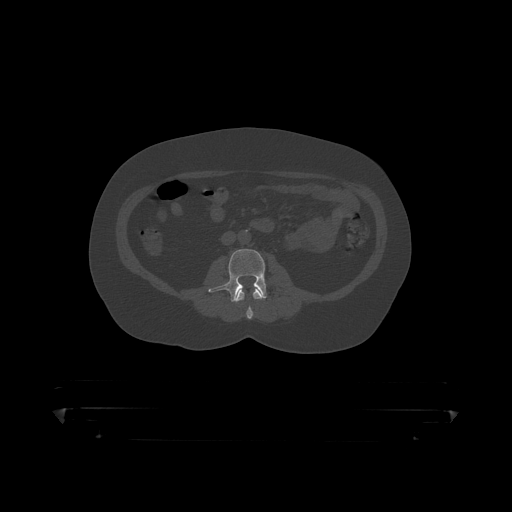
CT including the spine, one axial slice; position 98 of 390 along the scan axis; reconstruction kernel STANDARD; 120 kVp; bone window (W 1800 / L 400 HU); 512 × 512 image matrix. Patient: male, 60 years. Case-level facts recorded for this patient, not image findings: primary cancer: prostate.
Annotated regions visible in this slice (semi-automatically segmented with operator editing):
- L2 vertebra: bounding box <235,288,264,319> (left, top, right, bottom; pixels)
- L3 vertebra: <209,249,267,302>